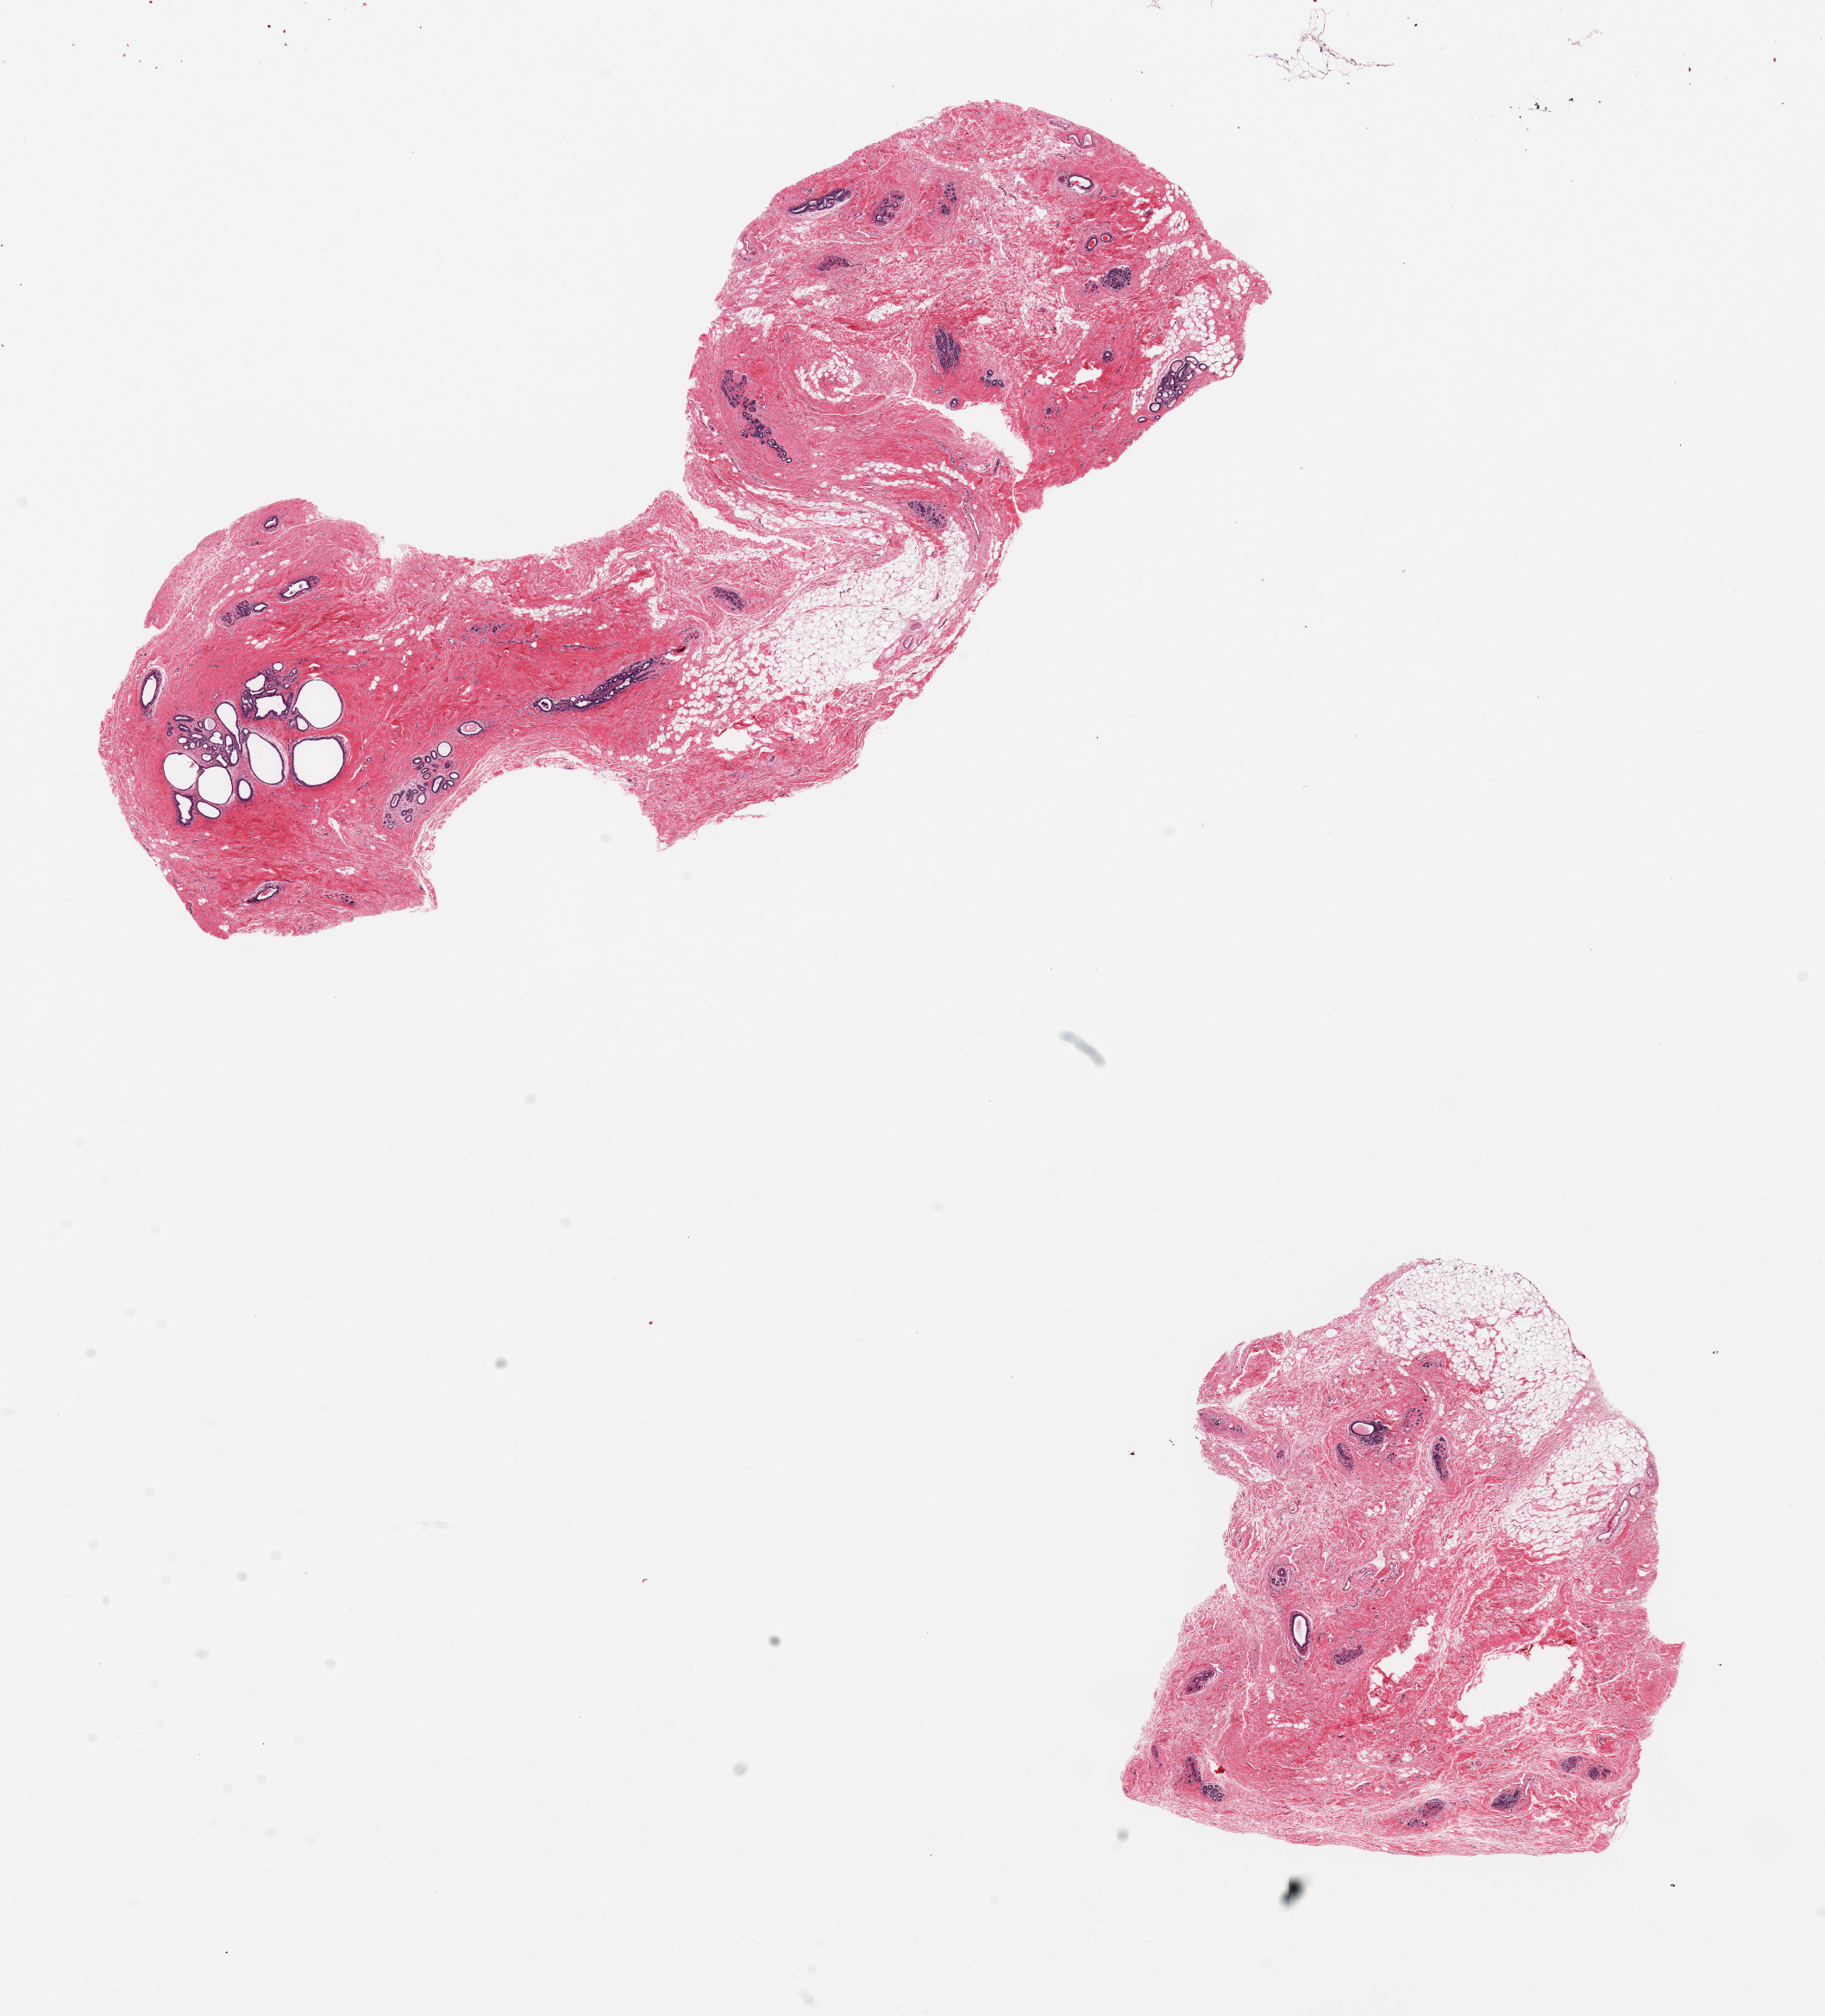
H&E whole-slide image, brightfield — whole scanned area (about 16.7 x 18.5 mm) shown as a low-resolution overview; PAXgene-fixed, paraffin-embedded tissue; target tissue: breast; tissue donor sample. Female donor.
Review note (as recorded): 2 aliquots, ~8x5mm; Focal areas of fibrocystic (microcystic) change; normal TDLUs en.